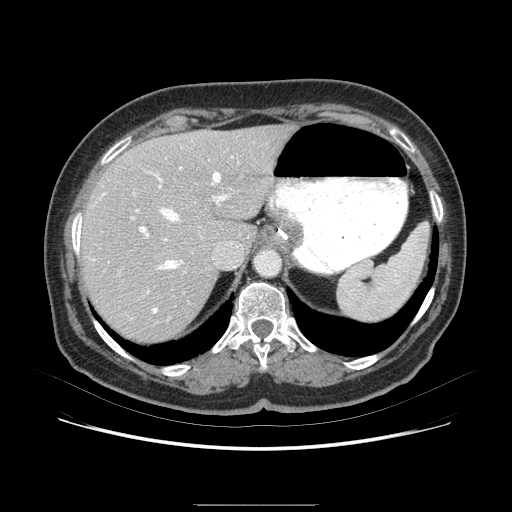
Contrast-enhanced abdominal CT (liver protocol), one axial slice. Slice 57 of 79 in the series (ordered by position). 120 kVp. Soft-tissue window (W 400 / L 40 HU). 2.5 mm slice thickness. 512 × 512 image matrix, field of view 380 × 380 mm. From the clinical record (not read from this slice): diagnosis: hepatocellular carcinoma (patient treated with transarterial chemoembolisation; whether this scan precedes or follows treatment is not stated here); TNM stage (as recorded): Stage-I; Child-Pugh class: A; tumour differentiation: poorly differentiated; tumour nodularity: uninodular.
Outlined on this slice (semi-automatic segmentation, software-assisted and operator-edited):
- abdominal aorta: bounding box <257,251,283,278> (left, top, right, bottom; pixels)
- liver parenchyma outside the tumour (the mass and vessels are separate outlines, so this box may not span the whole liver): <81,128,300,328>
- liver vessels: <131,159,242,248>